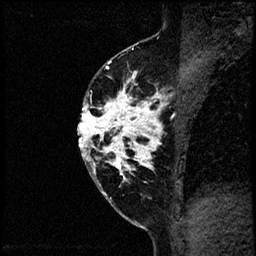
Breast MRI (dynamic contrast-enhanced), one sagittal slice. Slice 37 of 60 in the series (ordered by position). Dynamic contrast-enhanced study with each time point stored as its own series, time point 2 of 4 at this slice position (early post-contrast, ordered by acquisition time). 1.5 T. TE 4.2 ms, TR 17.6 ms. 2 mm slice thickness. 256 × 256 image matrix, field of view 200 × 200 mm. Patient: female, 40 years. From the clinical record (not read from this slice): setting: breast cancer imaged before/during neoadjuvant chemotherapy; receptor status: HER2-positive.
Outlined on this slice (semi-automatic segmentation, software-assisted and operator-edited):
- analysis volume of interest (the breast-tissue region the enhancement analysis was run in; not a lesion): bounding box <79,56,197,205> (left, top, right, bottom; pixels)
- tumour enhancement mask (voxels above the 100 % enhancement threshold inside the analysis volume of interest): <79,59,197,195>